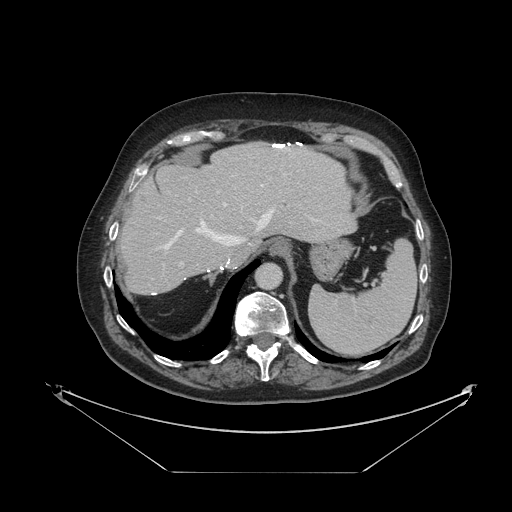
Contrast-enhanced abdominal CT, one axial slice; slice 86 of 121 in the series (ordered by position); 120 kVp; soft-tissue window (W 400 / L 40 HU); 512 × 512 image matrix. Male patient, age 68 years. From the clinical record (not read from this slice): diagnosis: colorectal cancer liver metastases, imaged before liver resection; multiple liver metastases: no; largest metastasis: 4 cm; chemotherapy before resection: yes.
Annotated regions visible in this slice (expert manual segmentation):
- hepatic veins: bounding box [x1, y1, x2, y2] px = [160, 185, 317, 250]
- liver: [121, 143, 356, 294]
- planned liver remnant (the part of the liver to remain after resection): [120, 143, 355, 294]
- portal vein (with intrahepatic branches): [179, 203, 227, 266]
- liver metastasis: [139, 195, 148, 205]